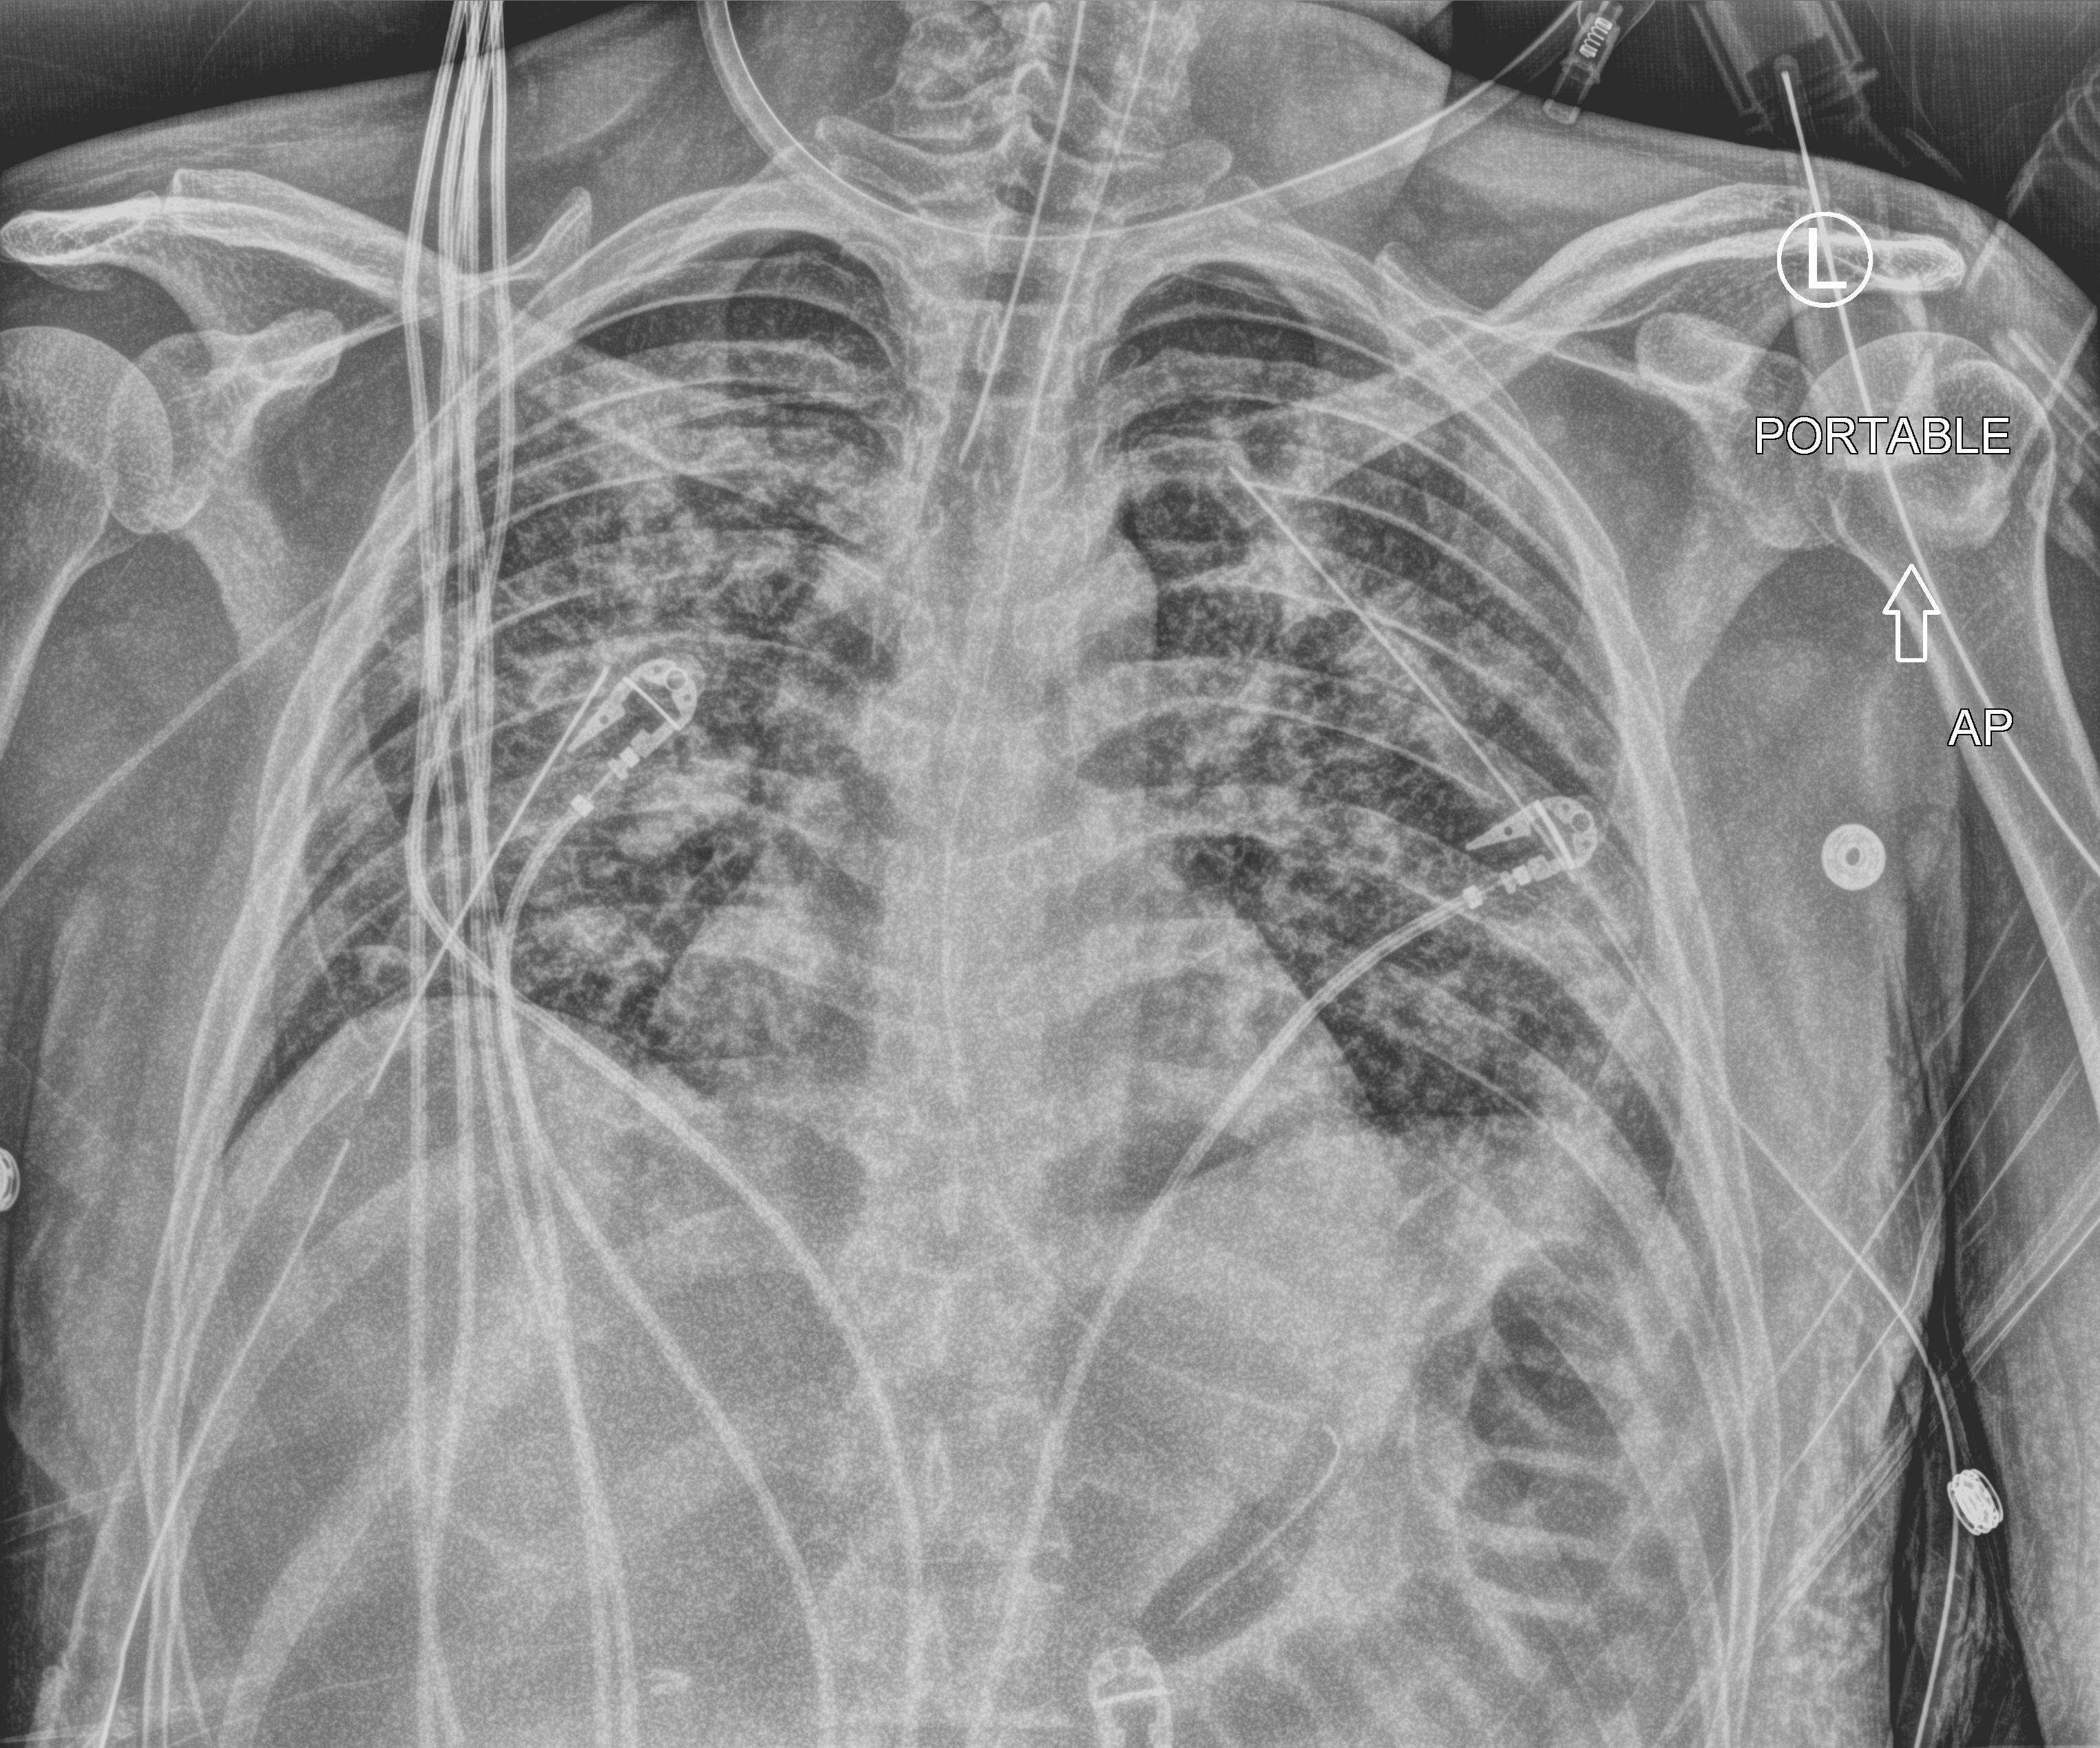
Portable chest radiograph; anteroposterior (AP) projection. Patient hospitalised with COVID-19; male, aged 18–59 years.
Hospital-stay facts (about this admission, not read from this image; timing relative to this image not recorded):
- admitted to intensive care during this hospital stay: yes
- other chronic lung disease (admission record): no
- chronic kidney disease (admission record): no